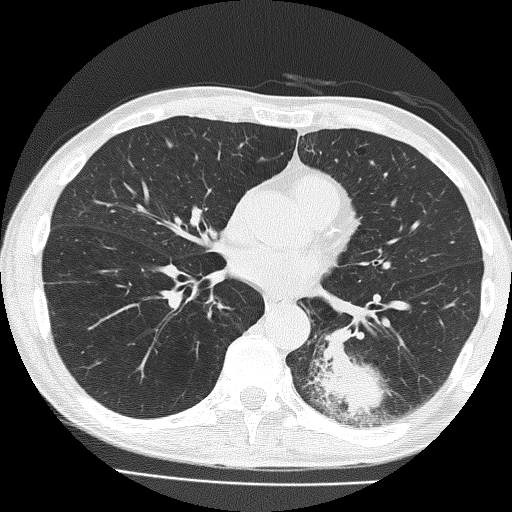
Low-dose screening chest CT, one axial slice; 120 kVp; lung window (W 1500 / L -600 HU); 512 × 512 image matrix, field of view 324 × 324 mm.
Annotated regions visible in this slice (outlined manually by an expert reader):
- lesion 1 (tumor, lower lobe of left lung): bounding box [x1, y1, x2, y2] px = [313, 329, 388, 416]